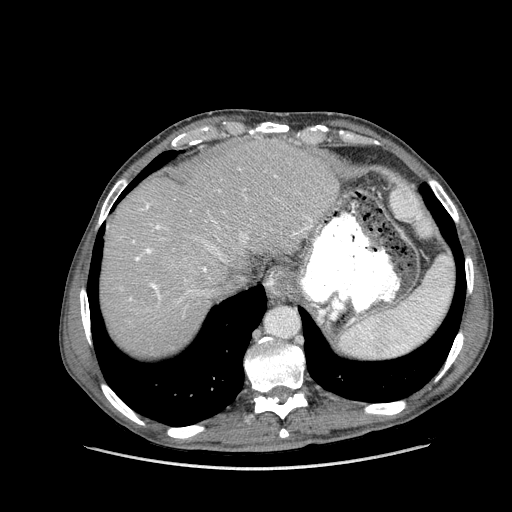
Contrast-enhanced abdominal CT (liver protocol), one axial slice. Position 123 of 162 along the scan axis. Reconstruction kernel STANDARD. Soft-tissue window (W 400 / L 40 HU). 2.5 mm slice thickness. 512 × 512 image matrix, field of view 400 × 400 mm. Case-level facts recorded for this patient, not image findings: diagnosis: hepatocellular carcinoma (patient treated with transarterial chemoembolisation; whether this scan precedes or follows treatment is not stated here); TNM stage (as recorded): Stage-IIIA; Child-Pugh class: A.
Structures marked on this image (semi-automatically segmented with operator editing):
- abdominal aorta: bounding box [x1, y1, x2, y2] px = [267, 308, 298, 337]
- liver parenchyma outside the tumour (the mass and vessels are separate outlines, so this box may not span the whole liver): [100, 138, 339, 356]
- liver vessels: [129, 203, 312, 301]